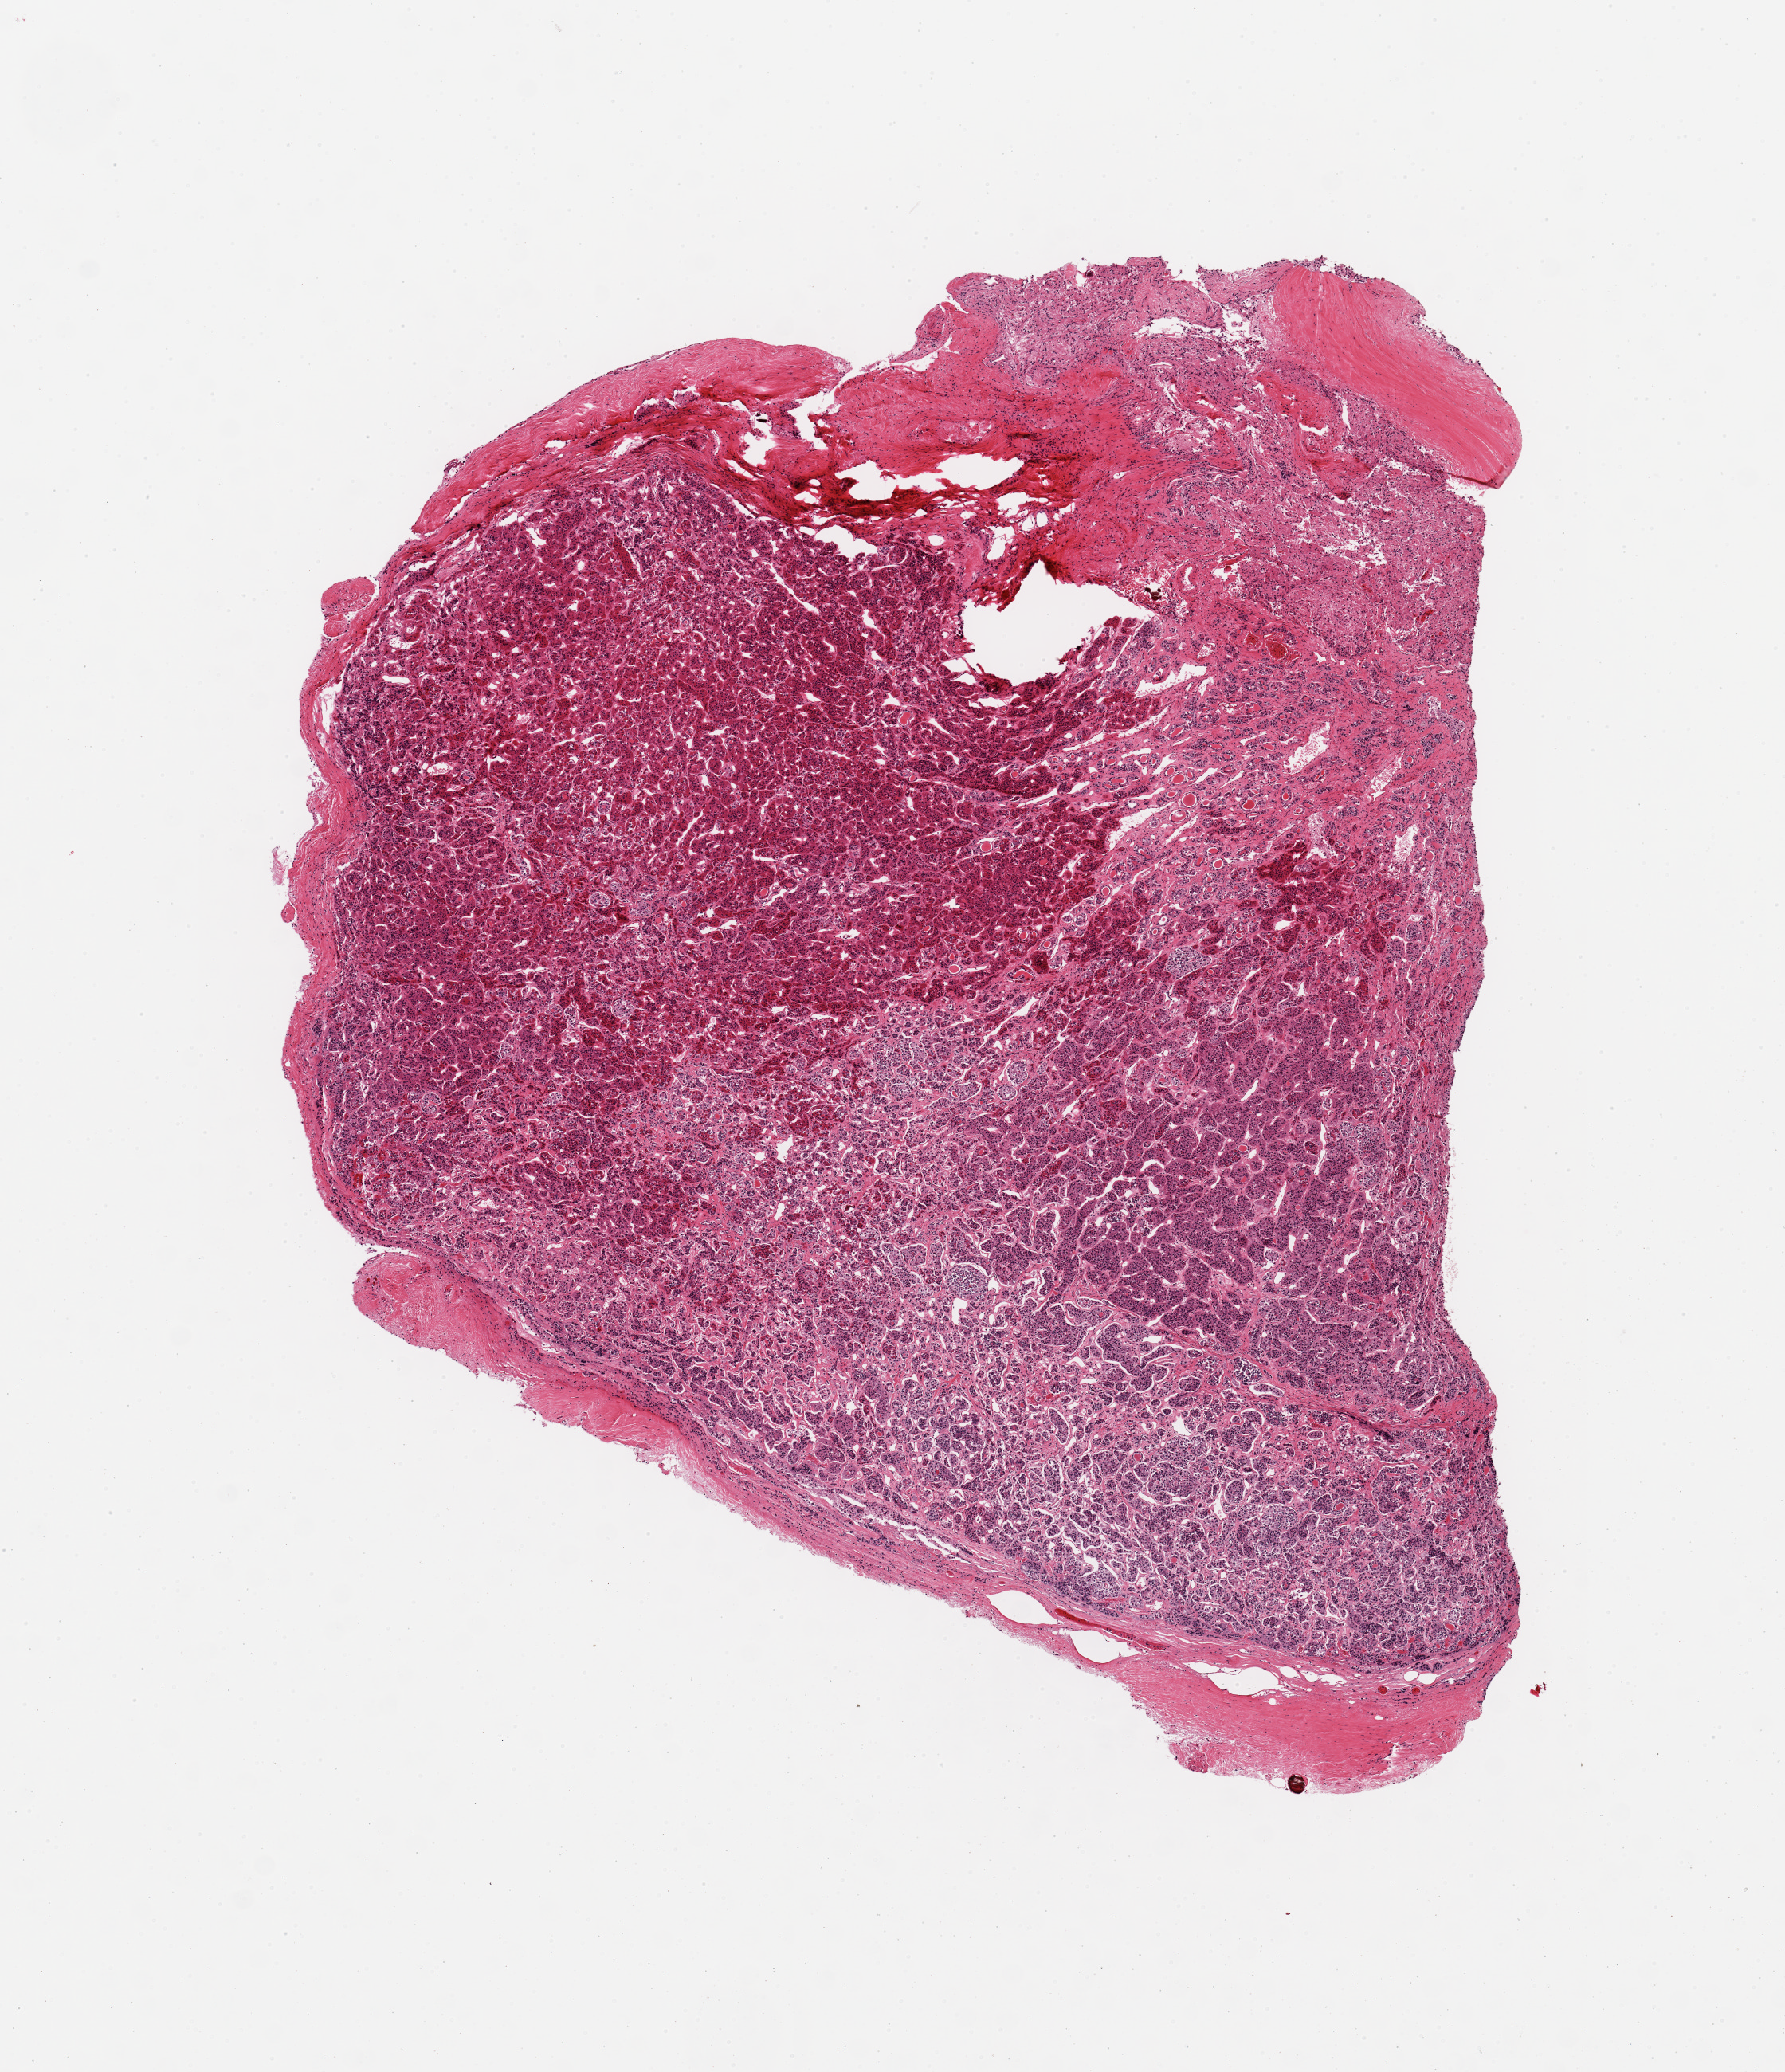
Digitized haematoxylin and eosin-stained section — whole scanned area (about 8.9 x 10.3 mm) shown as a low-resolution overview. PAXgene-fixed paraffin-embedded (PFPE) section. Sampled site (target tissue): pituitary. Tissue donor sample. Male donor.
* review note (as recorded): 1 piece, adhenohypophysis and focal dura